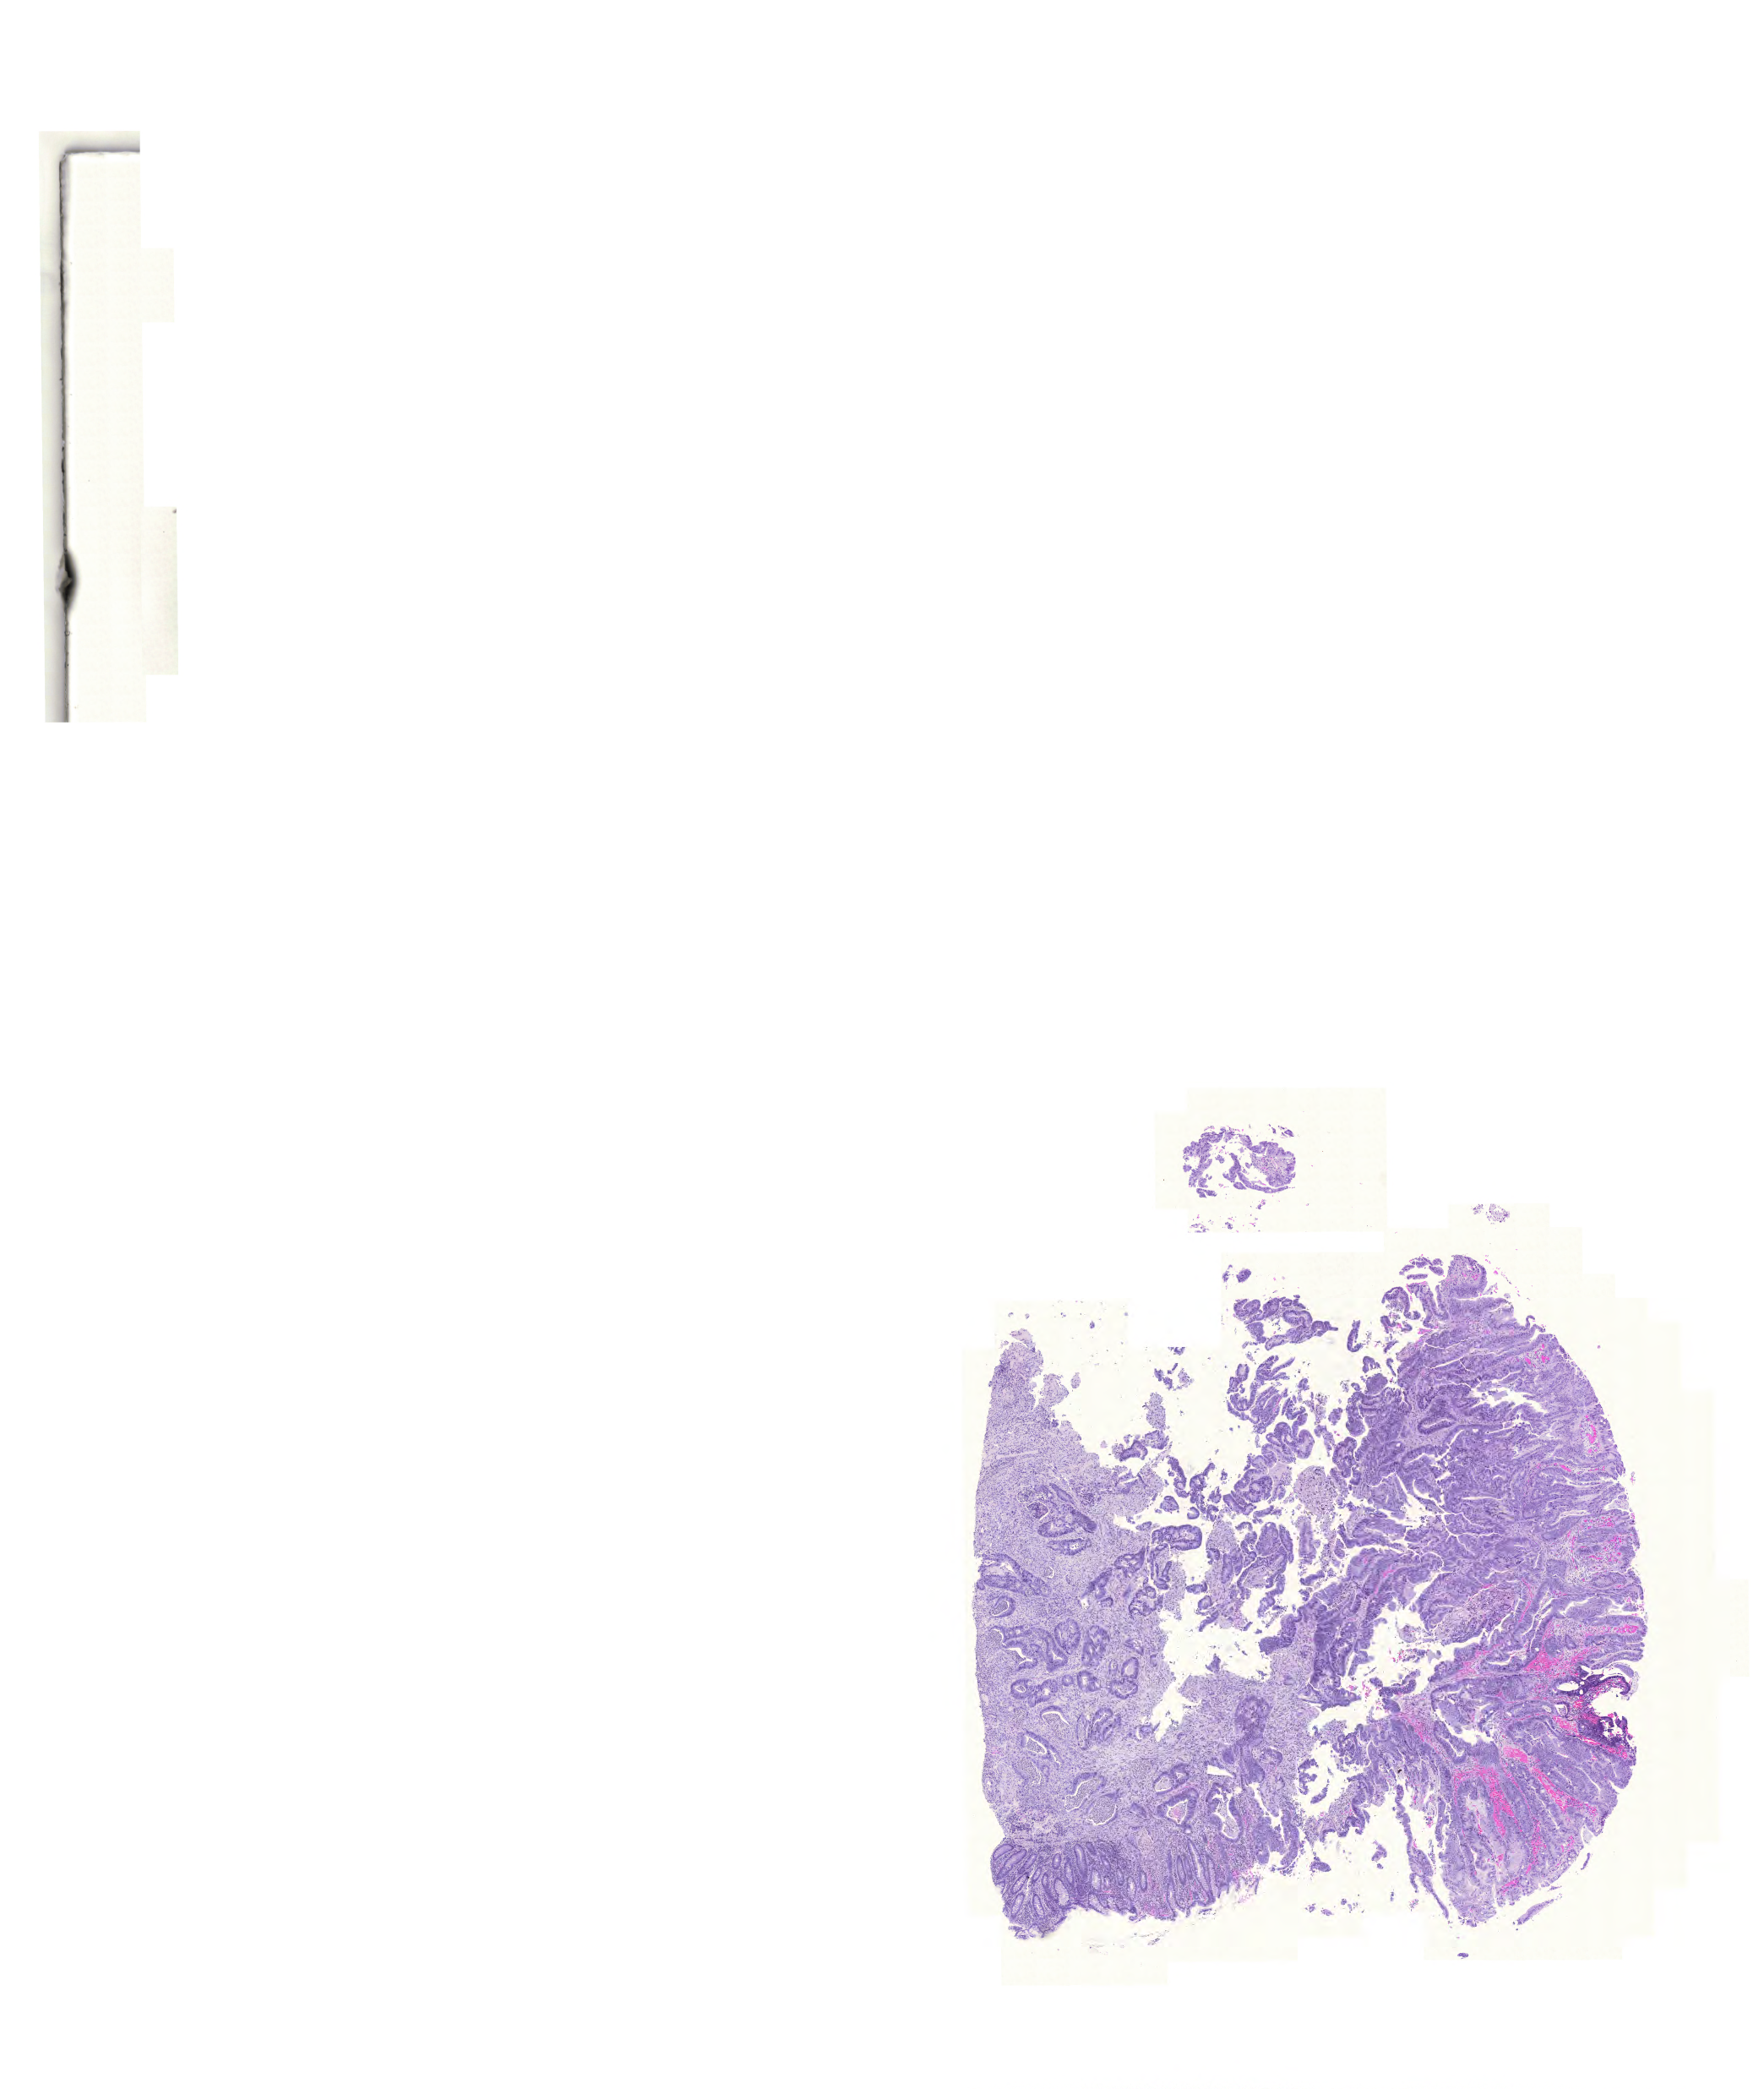
Digitized H&E tissue section (whole slide) — a low-resolution overview of the entire scanned area, about 15.5 x 18.4 mm (slide scanned at 20x), formalin-fixed paraffin-embedded (FFPE) diagnostic section, sample: primary tumour, colon. Patient: male, age at initial diagnosis 83 years.
Diagnosis: Adenocarcinoma, NOS.